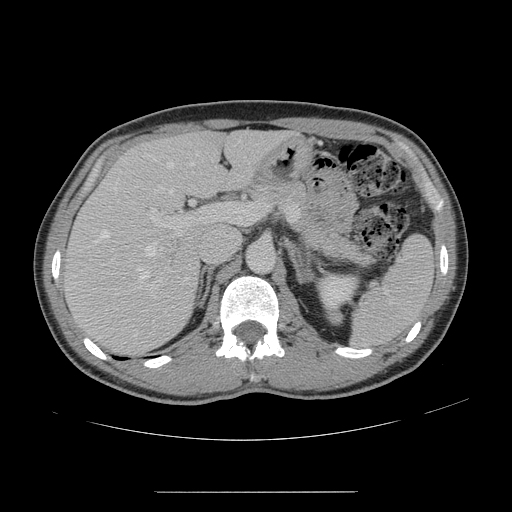
Contrast-enhanced abdominal CT, one axial slice; slice 91 of 178 in the series (ordered by position); 120 kVp; intravenous contrast given; soft-tissue window (W 400 / L 40 HU); 2.5 mm slice thickness; 512 × 512 image matrix, field of view 401 × 401 mm. Male patient, age 53 years. From the clinical record (not read from this slice): diagnosis: colorectal cancer liver metastases, imaged before liver resection.
Outlined on this slice (manually delineated by an expert):
- hepatic veins: bounding box [x1, y1, x2, y2] px = [95, 153, 198, 283]
- liver: [67, 130, 284, 353]
- planned liver remnant (the part of the liver to remain after resection): [149, 131, 283, 193]
- portal vein (with intrahepatic branches): [150, 203, 266, 289]